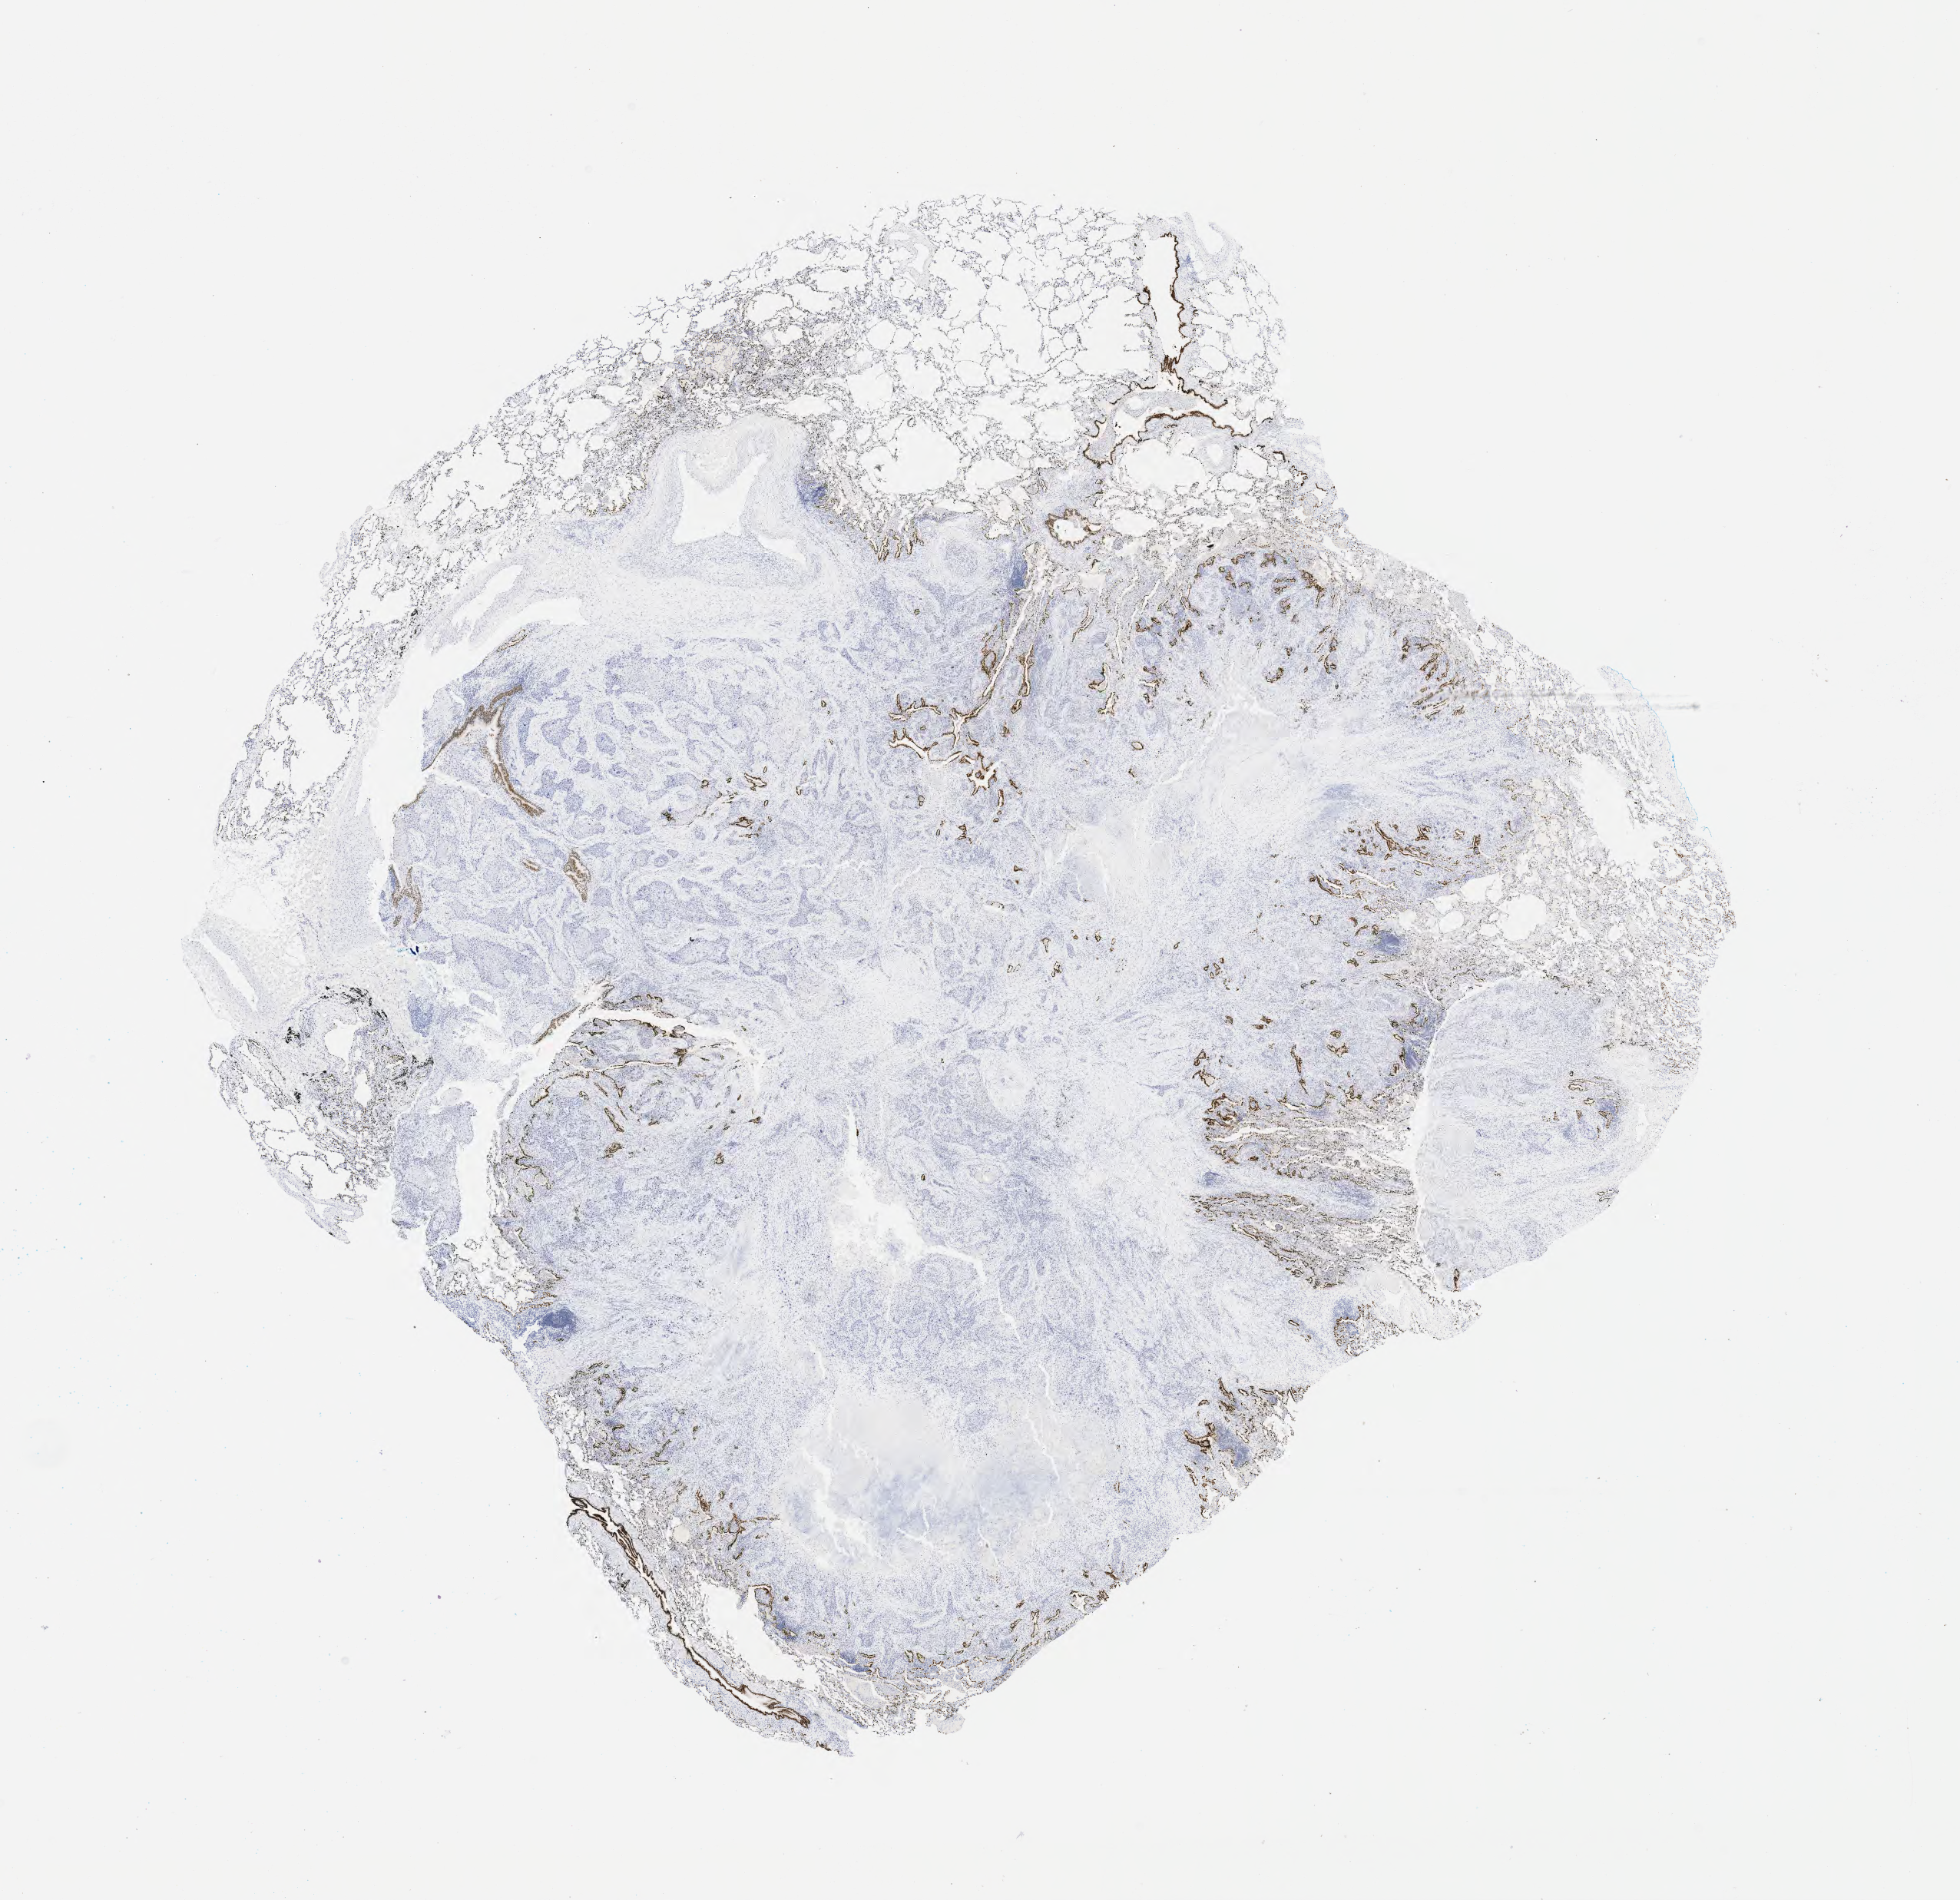
Immunohistochemistry (IHC) whole-slide image stained for TTF-1 (thyroid transcription factor 1) — a low-resolution overview of the entire scanned area, about 20.6 x 20.0 mm. Patient sex: male.
Specimen: tumor tissue; site: lower respiratory tract.